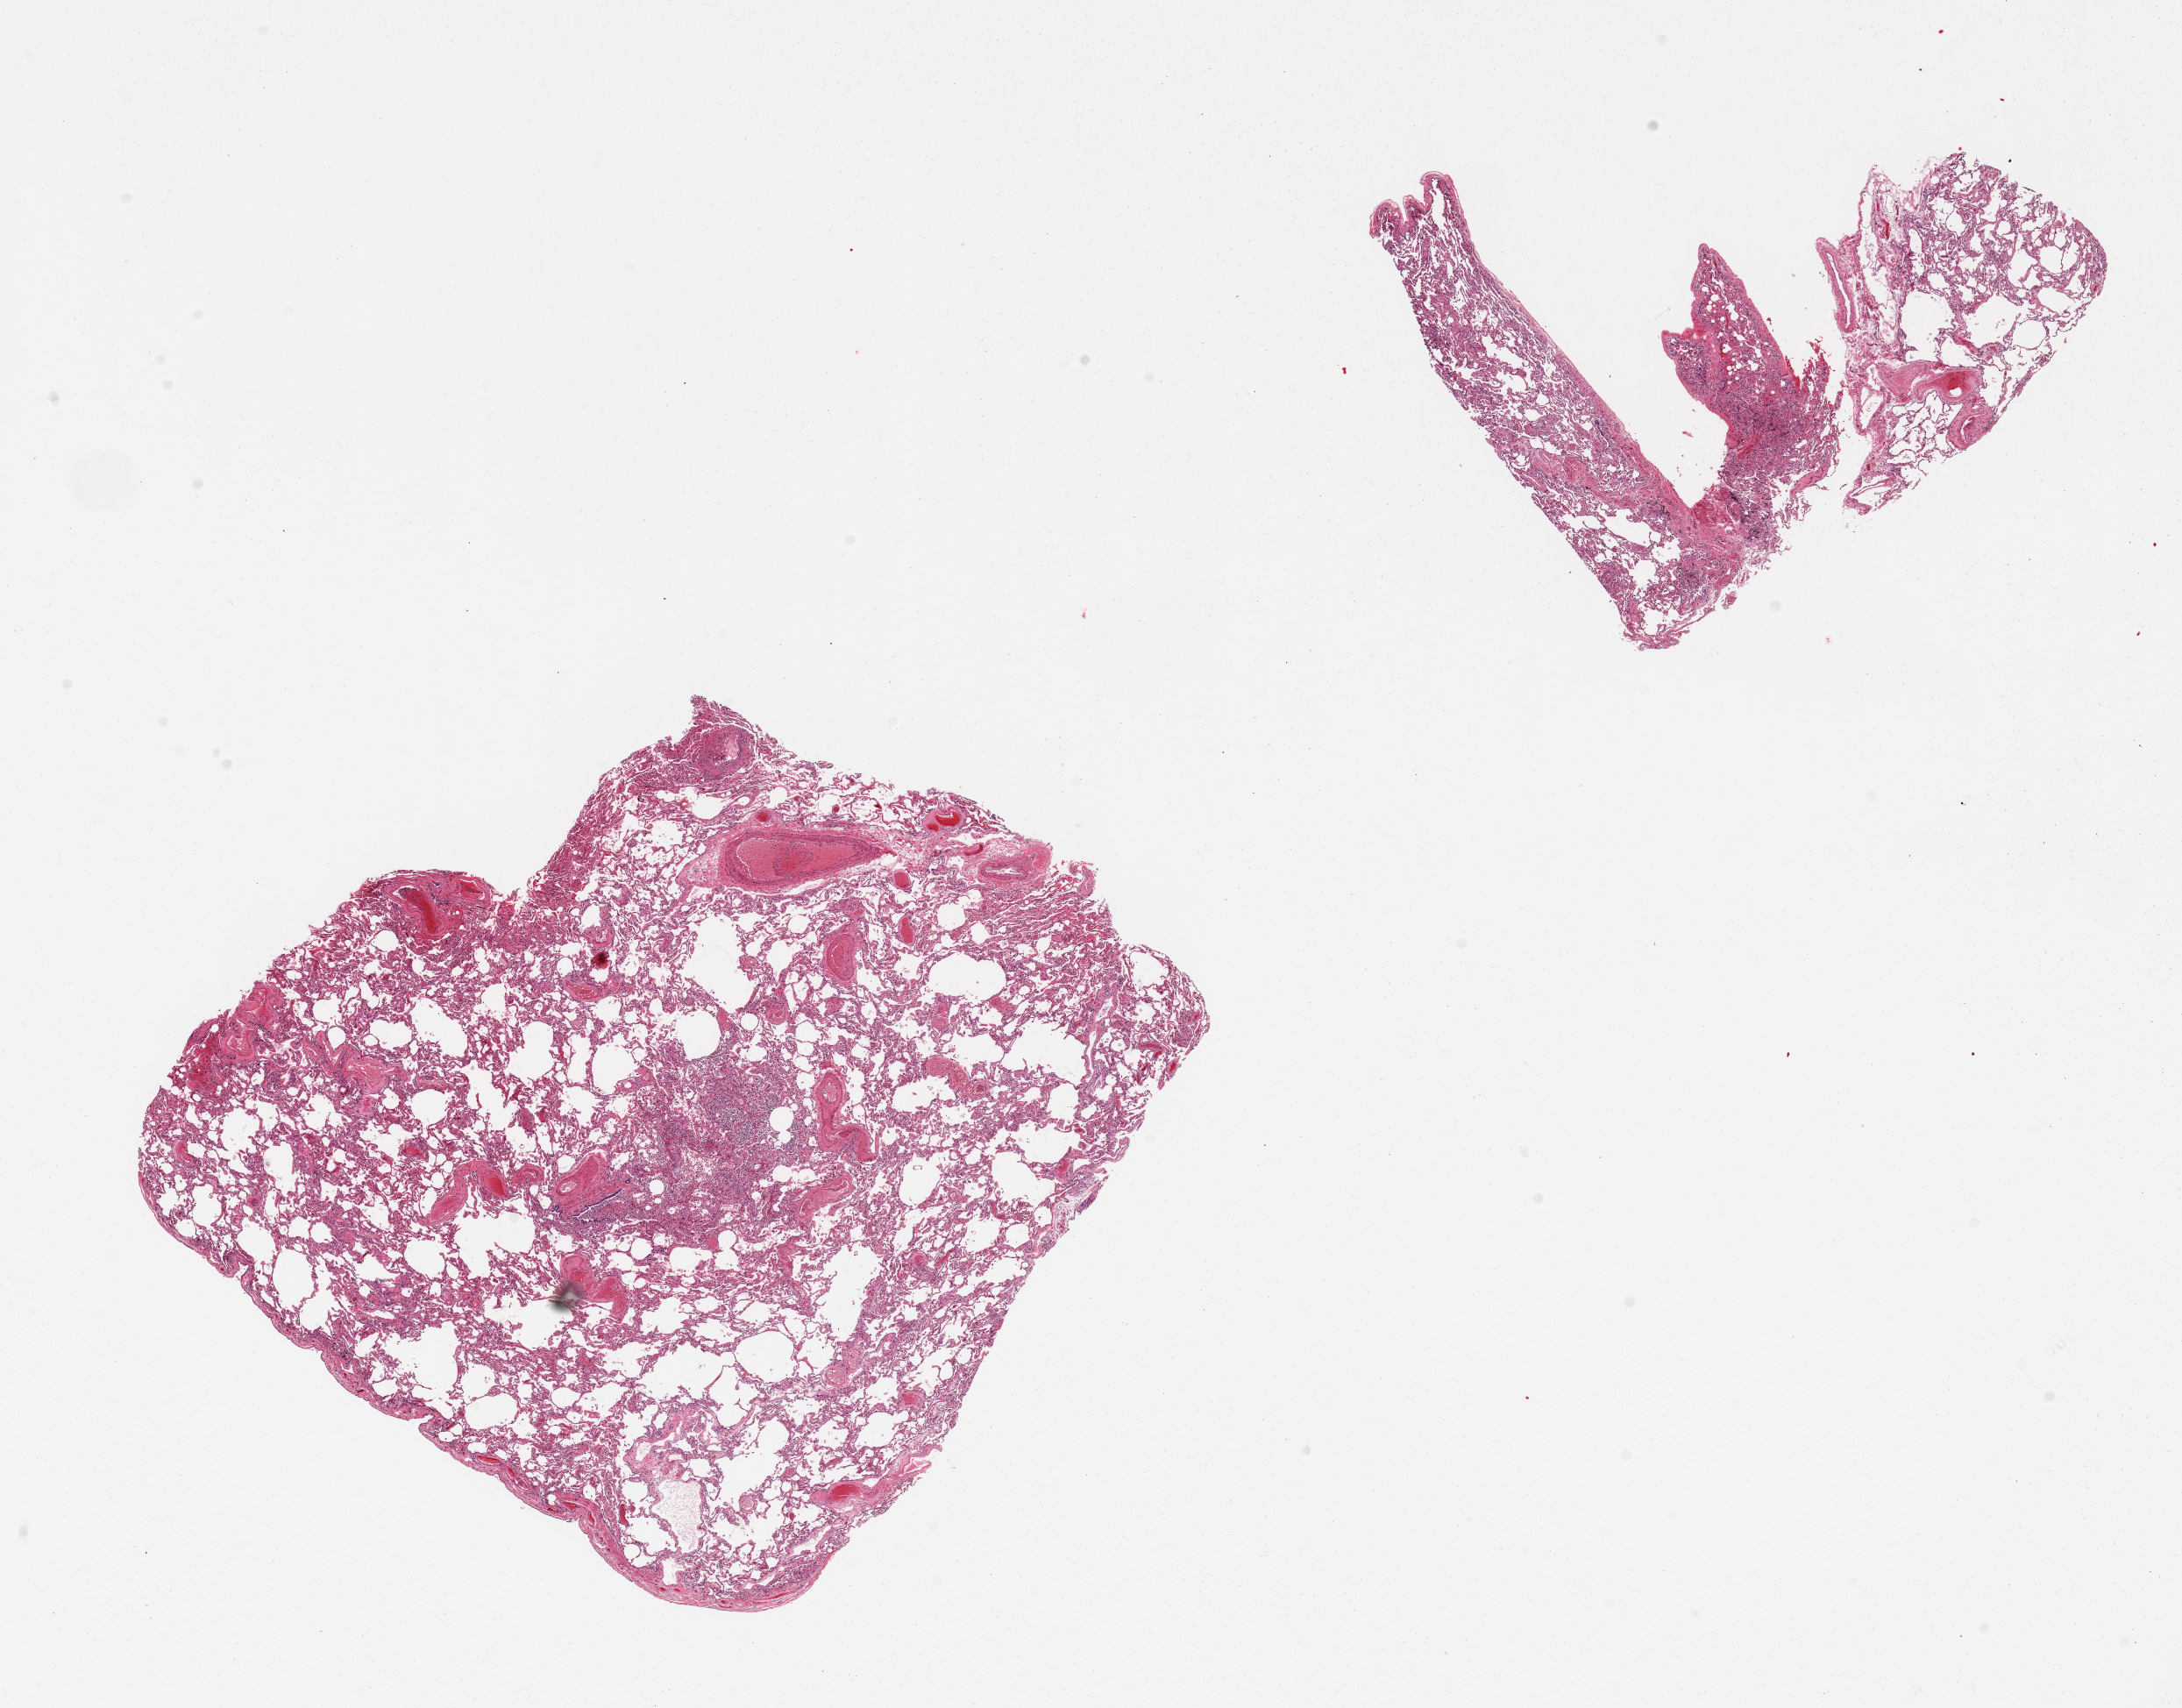
Digitized hematoxylin and eosin (H&E)-stained section — low-resolution overview of the scanned area, about 19.7 x 15.4 mm; PAXgene-fixed, paraffin-embedded tissue; target tissue: lung; donor tissue sample. Male donor.
Reviewer comment on this tissue sample: 2 pieces, patchy acute pneumonia/peribronchitis.